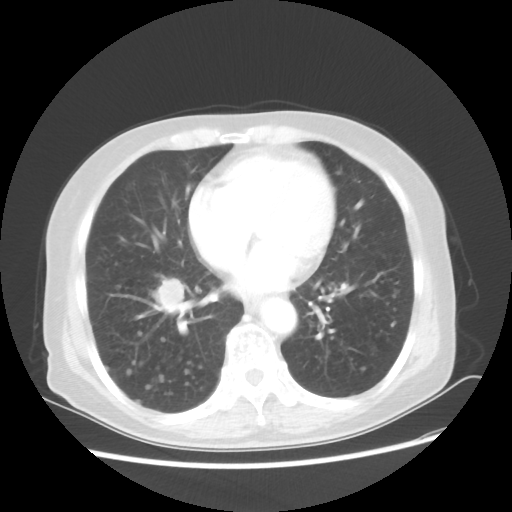
Chest CT, one axial slice. Reconstruction kernel STANDARD. Lung window (W 1500 / L -600 HU). 512 × 512 image matrix, field of view 360 × 360 mm. Female patient, age 68 years. From the clinical record (not read from this slice): clinical TNM (as recorded): T1c N3 M0.
Structures marked on this image (bounding box drawn by a radiologist):
- lung tumour (recorded histology: squamous cell carcinoma): box from (x=152, y=273) to (x=197, y=327) px